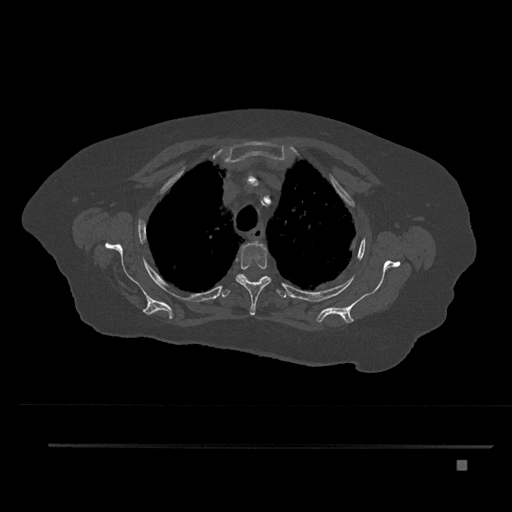
CT including the spine, one axial slice. Position 631 of 797 along the scan axis. Reconstruction kernel Br40s/3. Bone window (W 1800 / L 400 HU). 0.5 mm slice thickness. 512 × 512 image matrix, field of view 437 × 437 mm. Patient: female, 76 years. Case-level facts recorded for this patient, not image findings: primary cancer: lung; vertebrae with lytic lesions (as recorded): T11, L3.
Outlined on this slice (semi-automatic segmentation, software-assisted and operator-edited):
- T2 vertebra: bounding box <255,241,259,243> (left, top, right, bottom; pixels)
- T3 vertebra: <235,241,271,316>
- T4 vertebra: <220,274,287,298>